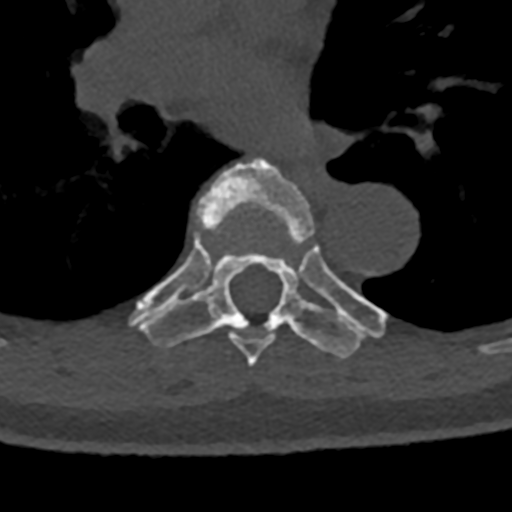
CT including the spine, one axial slice. Position 781 of 797 along the scan axis. Bone window (W 1800 / L 400 HU). 0.5 mm slice thickness. 512 × 512 image matrix, field of view 160 × 160 mm. Male patient, age 74 years. Case-level facts recorded for this patient, not image findings: primary cancer: renal.
Structures marked on this image (semi-automatically segmented with operator editing):
- T6 vertebra: bounding box <172,158,315,367> (left, top, right, bottom; pixels)
- T7 vertebra: <129,235,385,359>